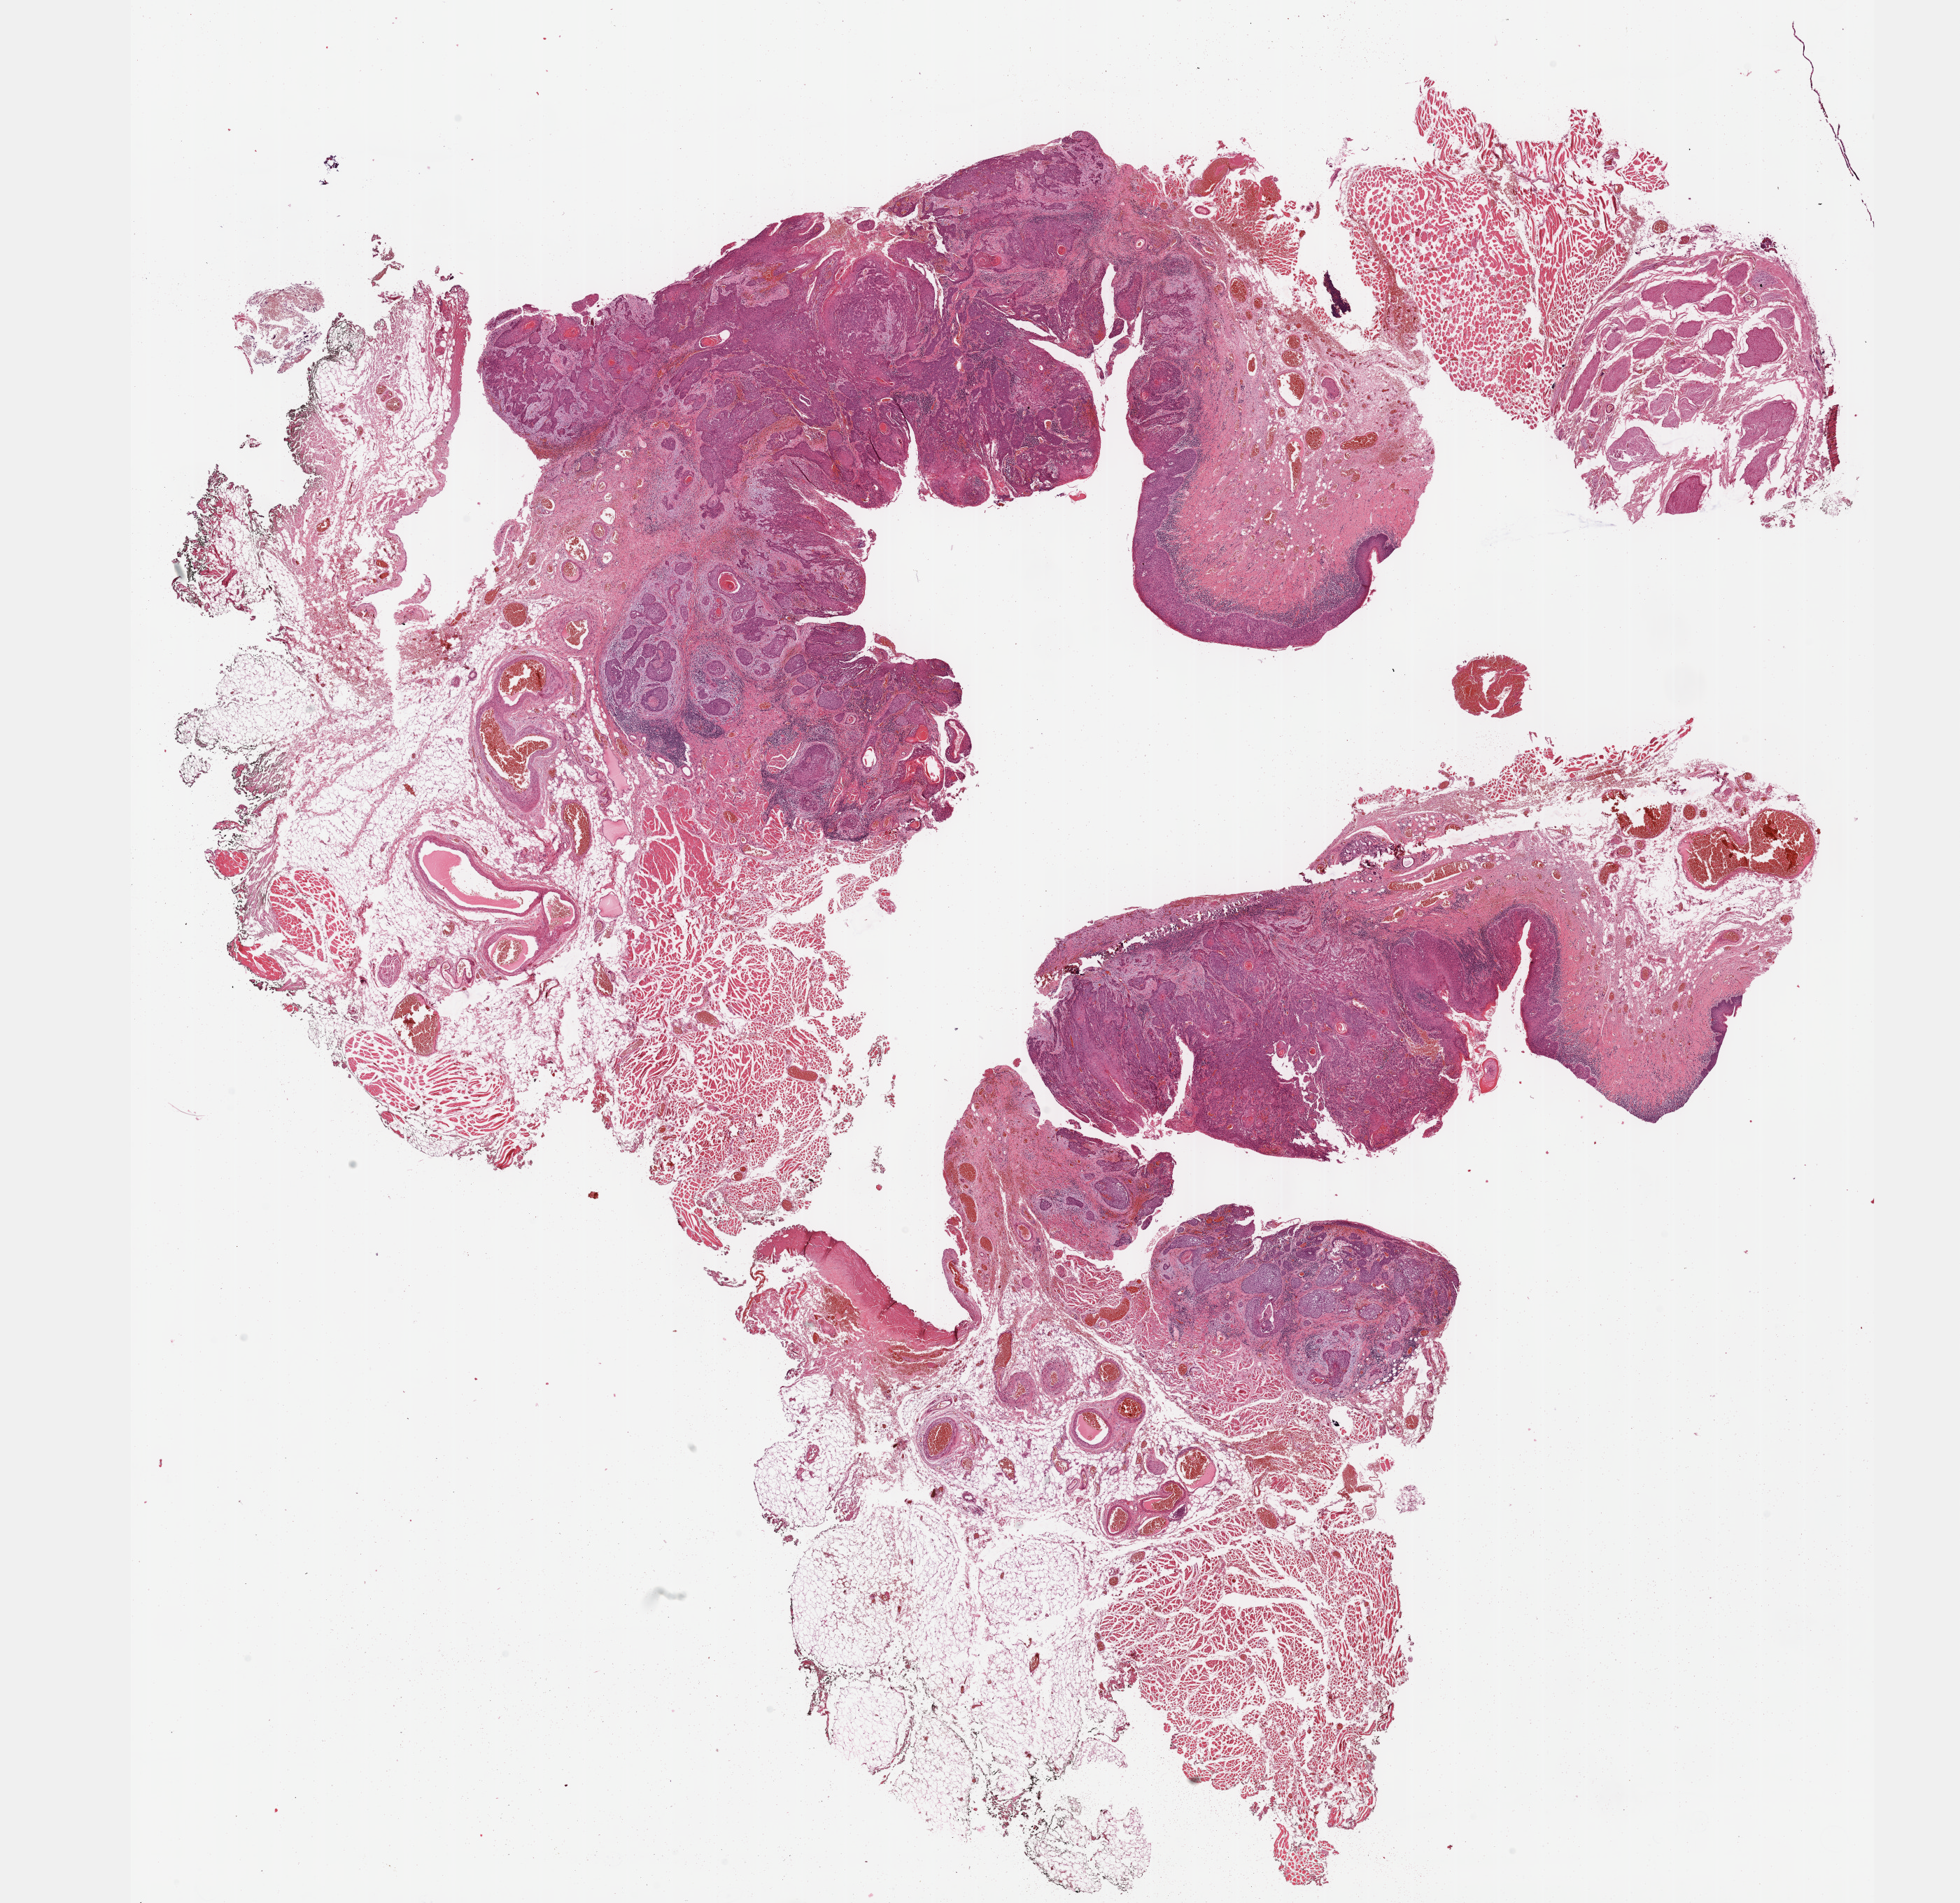
H&E-stained whole-slide image, shown as a low-resolution overview of the whole scanned area (about 22.6 x 22.0 mm, from a 40x scan). Formalin-fixed paraffin-embedded (FFPE) diagnostic section. Primary tumour sample from the head and neck. Female, age 79 years at initial diagnosis. Histologic grade: G2 (moderately differentiated).
* AJCC pathologic stage: IVA (6th edition)
* pathologic diagnosis: Squamous cell carcinoma, NOS (floor of mouth, NOS)